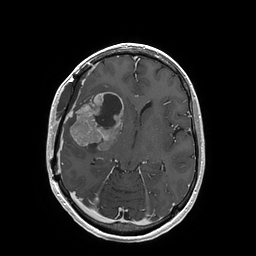
Brain MRI from a brain-tumour surgery series, one axial slice; T1-weighted post-contrast; 1 mm slice thickness; 256 × 256 image matrix, field of view 250 × 250 mm. Case-level facts recorded for this patient, not image findings: histopathology: Glioblastoma; WHO grade: 4; IDH mutation: no; tumour location: Right Insular.
Outlined on this slice (expert manual segmentation):
- tumour: bounding box (x1, y1, x2, y2) in pixels: (69, 92, 123, 151)